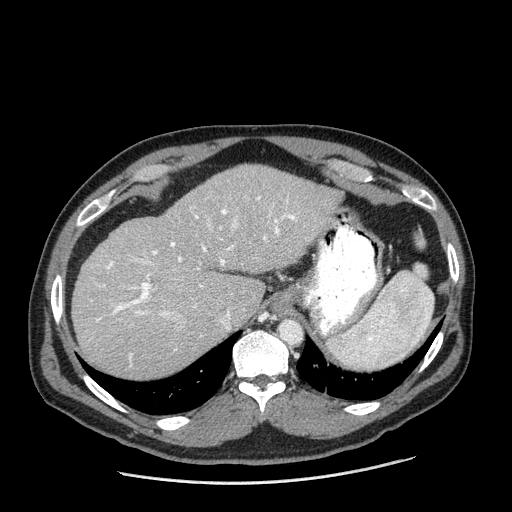
Contrast-enhanced abdominal CT (liver protocol), one axial slice; reconstruction kernel STANDARD; 120 kVp; one of 2 acquisitions stored at this slice position; soft-tissue window (W 400 / L 40 HU); 2.5 mm slice thickness; 512 × 512 image matrix, field of view 400 × 400 mm. Case-level facts recorded for this patient, not image findings: diagnosis: hepatocellular carcinoma (patient treated with transarterial chemoembolisation; whether this scan precedes or follows treatment is not stated here); TNM stage (as recorded): Stage-II; Child-Pugh class: A; tumour differentiation: moderately differentiated.
Structures marked on this image (semi-automatic segmentation, software-assisted and operator-edited):
- liver parenchyma outside the tumour (the mass and vessels are separate outlines, so this box may not span the whole liver): bounding box (x1, y1, x2, y2) in pixels: (72, 164, 340, 378)
- liver vessels: (96, 196, 299, 359)